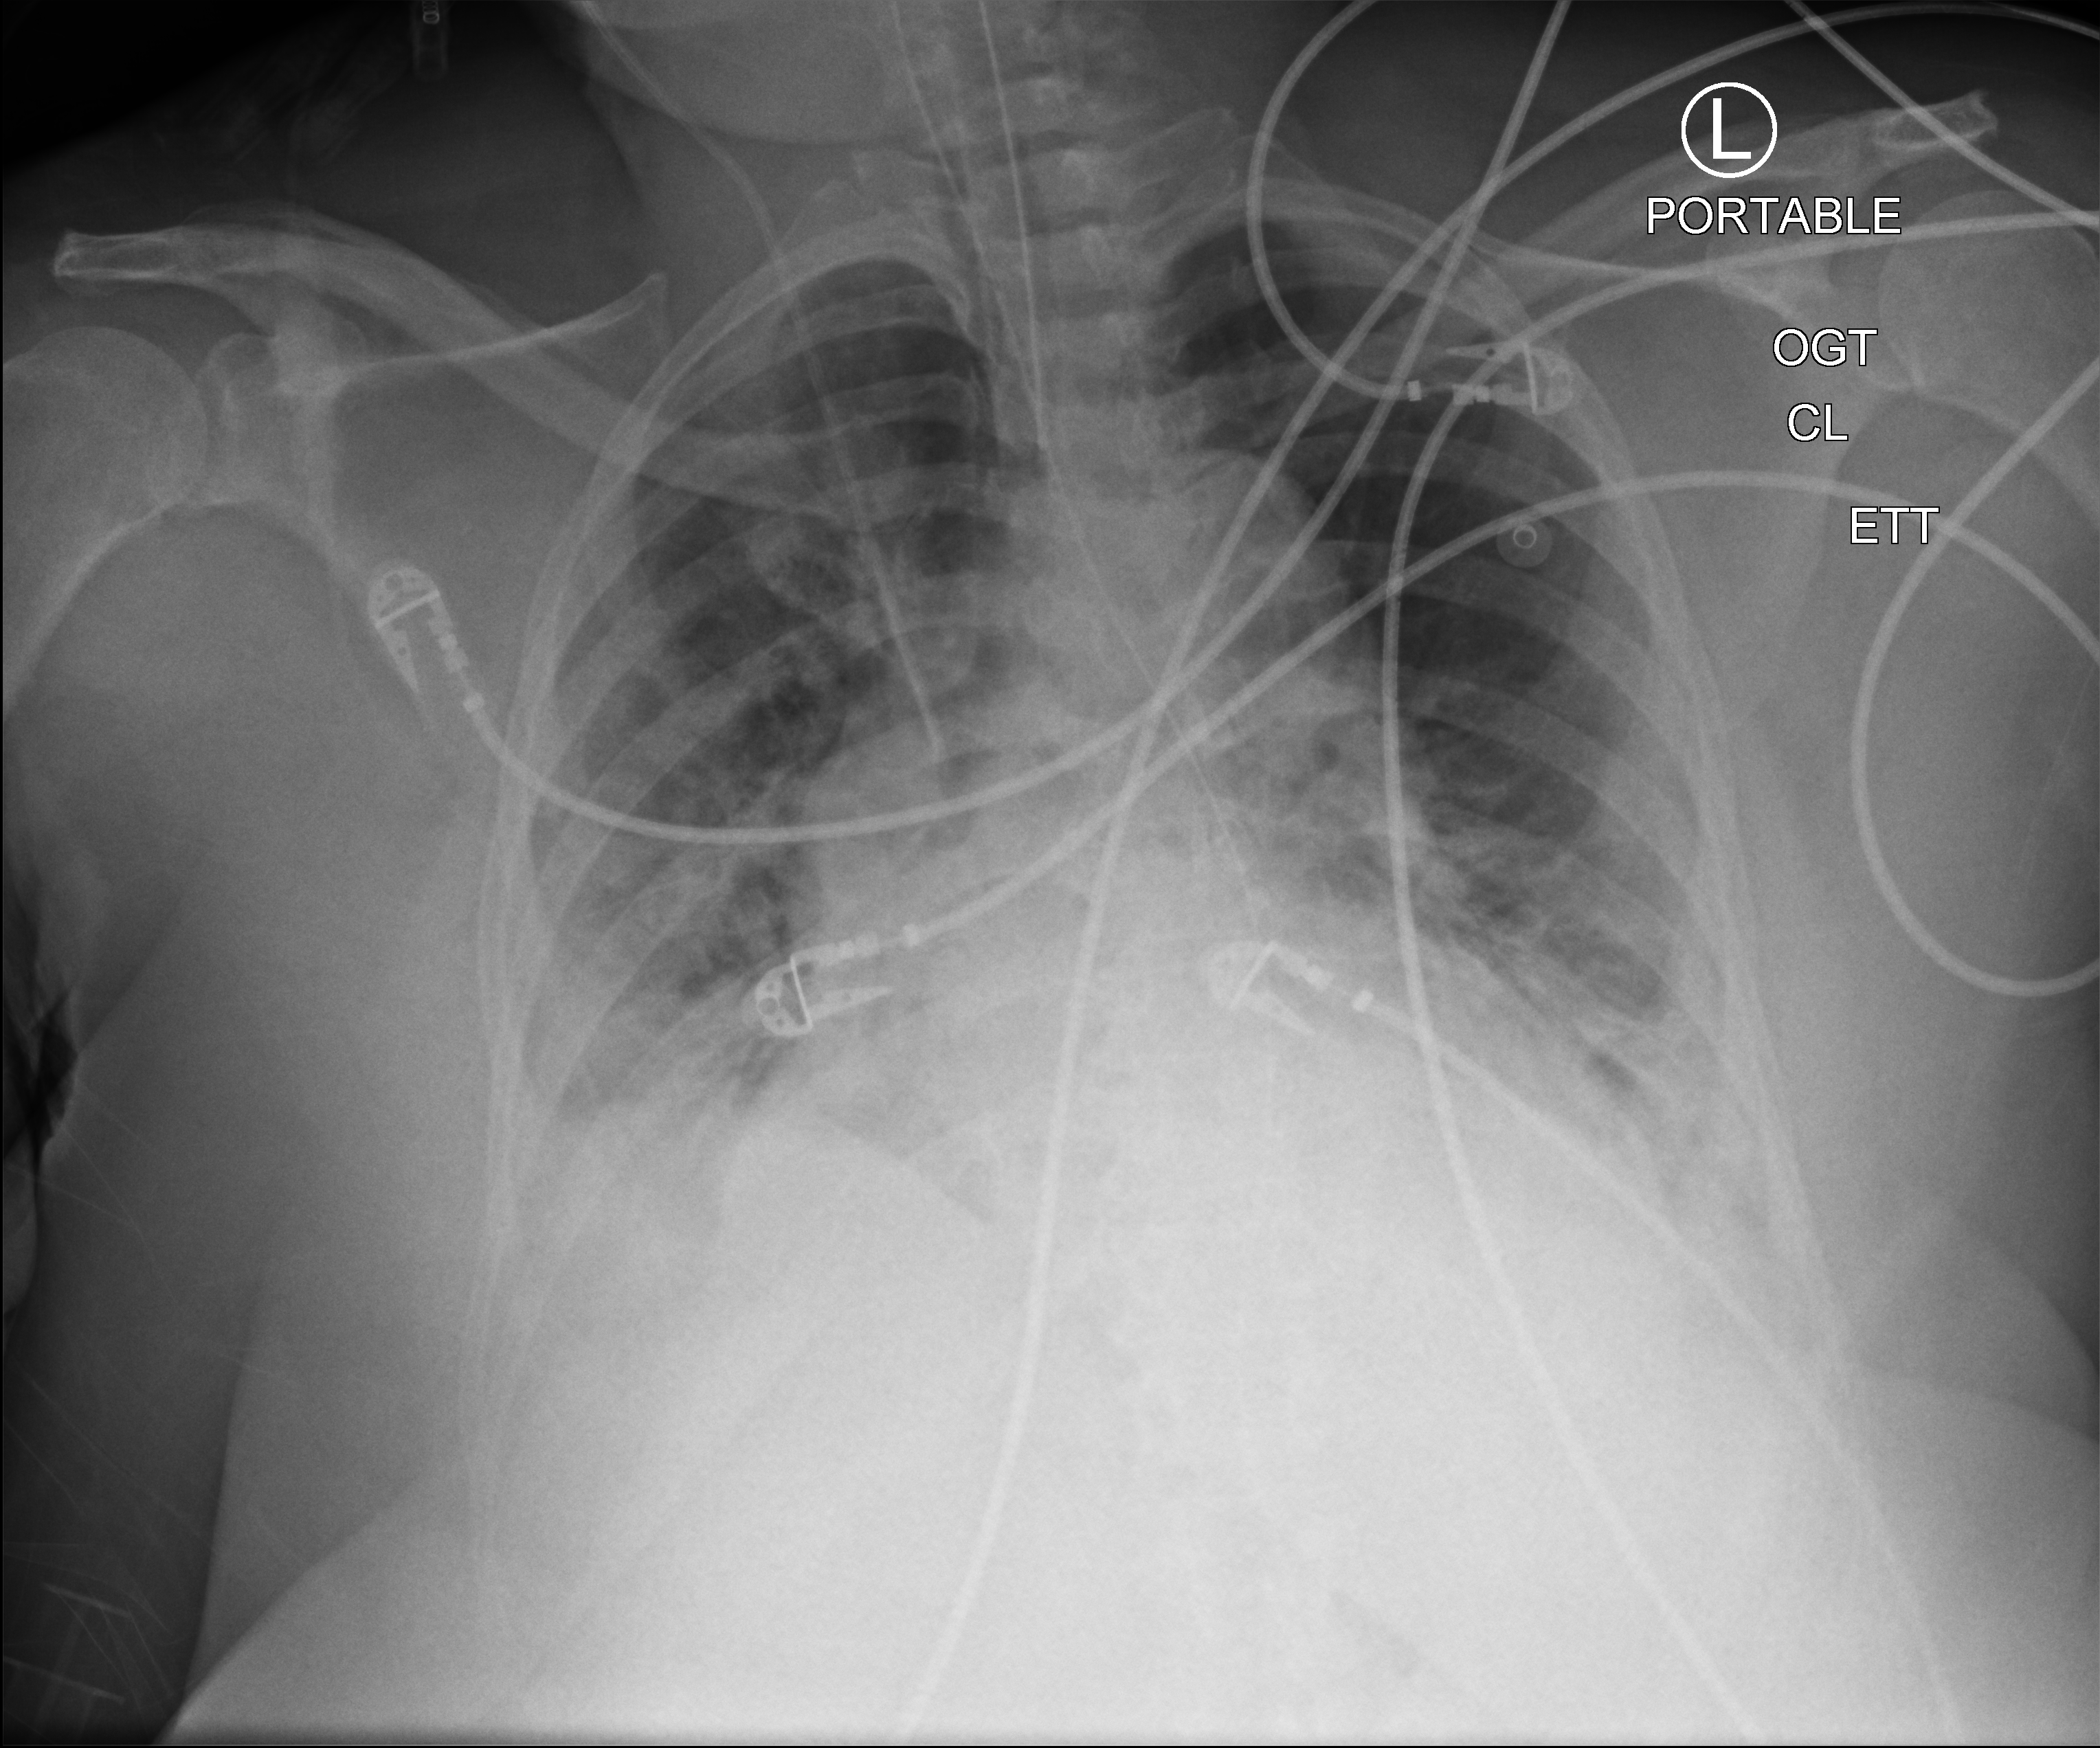
Chest X-ray (portable), anteroposterior (AP) projection. Patient hospitalised with COVID-19; female, aged 60–74 years.
Admission-level facts for this patient (not findings on this image; timing relative to this image not recorded):
- admitted to intensive care during this hospital stay: yes
- mechanically ventilated during this hospital stay: yes